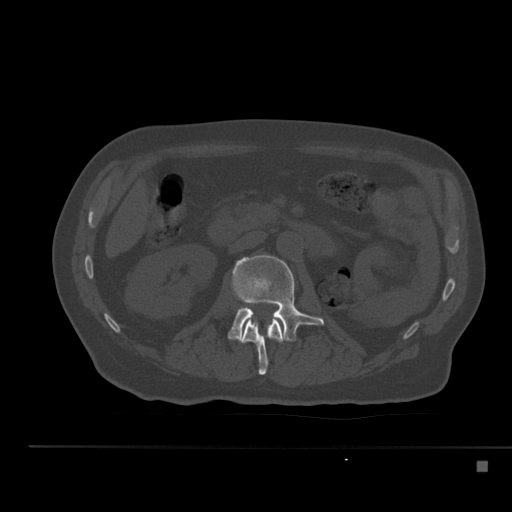
CT including the spine, one axial slice. Slice 194 of 517 in the series (ordered by position). Bone window (W 1800 / L 400 HU). 512 × 512 image matrix, field of view 408 × 408 mm. Patient: male, 70 years. From the clinical record (not read from this slice): primary cancer: renal; vertebrae with lytic lesions (as recorded): T4, T6, T10, T12, L3, L4, L5.
Structures marked on this image (semi-automatic segmentation, software-assisted and operator-edited):
- L1 vertebra: bounding box (x1, y1, x2, y2) in pixels: (239, 317, 286, 375)
- L2 vertebra: (228, 254, 324, 342)